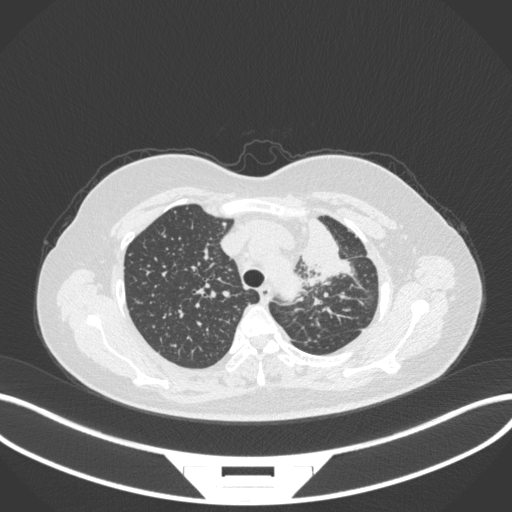
Chest CT, one axial slice; position 259 of 348 along the scan axis; reconstruction kernel B31f; lung window (W 1500 / L -600 HU); 512 × 512 image matrix. Patient: female, 49 years. Case-level facts recorded for this patient, not image findings: clinical TNM (as recorded): T1c N0 M1.
Structures marked on this image (rectangle marked by the reading radiologist):
- lung tumour (recorded histology: adenocarcinoma): bounding box [x1, y1, x2, y2] px = [290, 206, 353, 284]